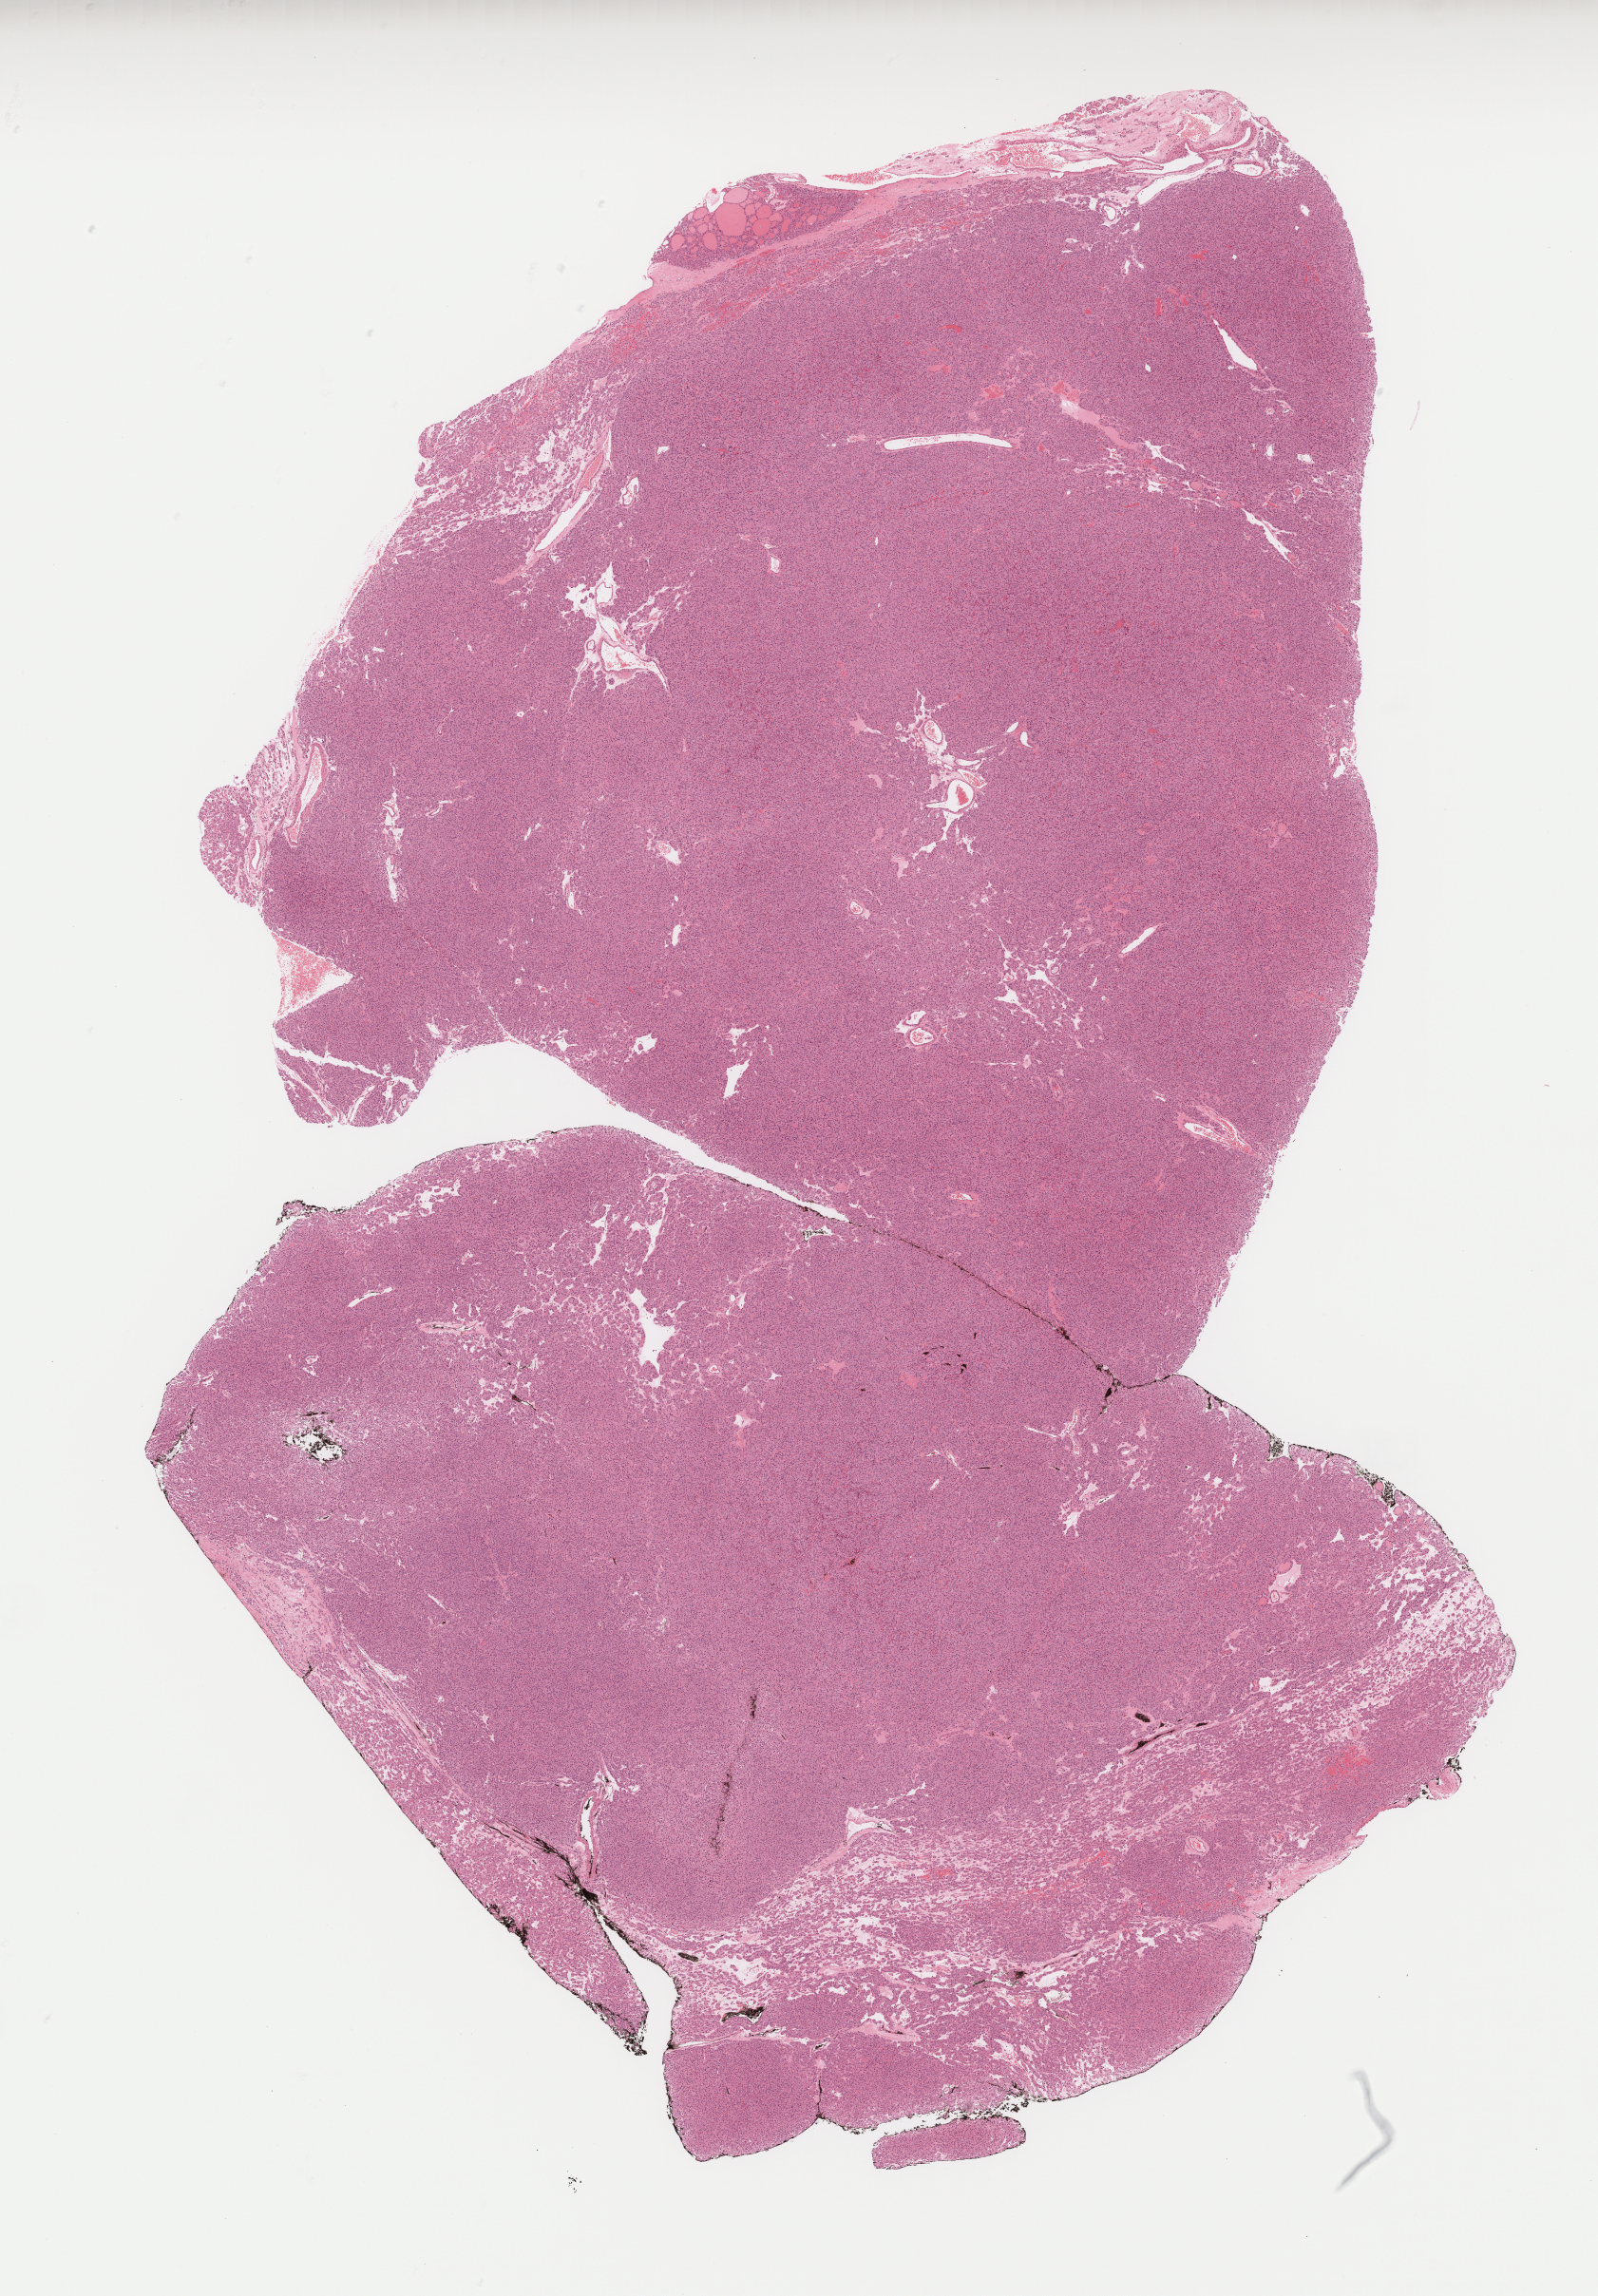
Digitized H&E tissue section (whole slide) — whole scanned area (about 13.5 x 19.5 mm) shown as a low-resolution overview, formalin-fixed paraffin-embedded (FFPE) diagnostic section, sample: primary tumour, thyroid. Patient: female, age at initial diagnosis 56 years.
Diagnosis: Papillary carcinoma, follicular variant. AJCC pathologic stage: II (7th edition). Lymph nodes positive (case pathology): 0 of 1 examined. Laterality: left.